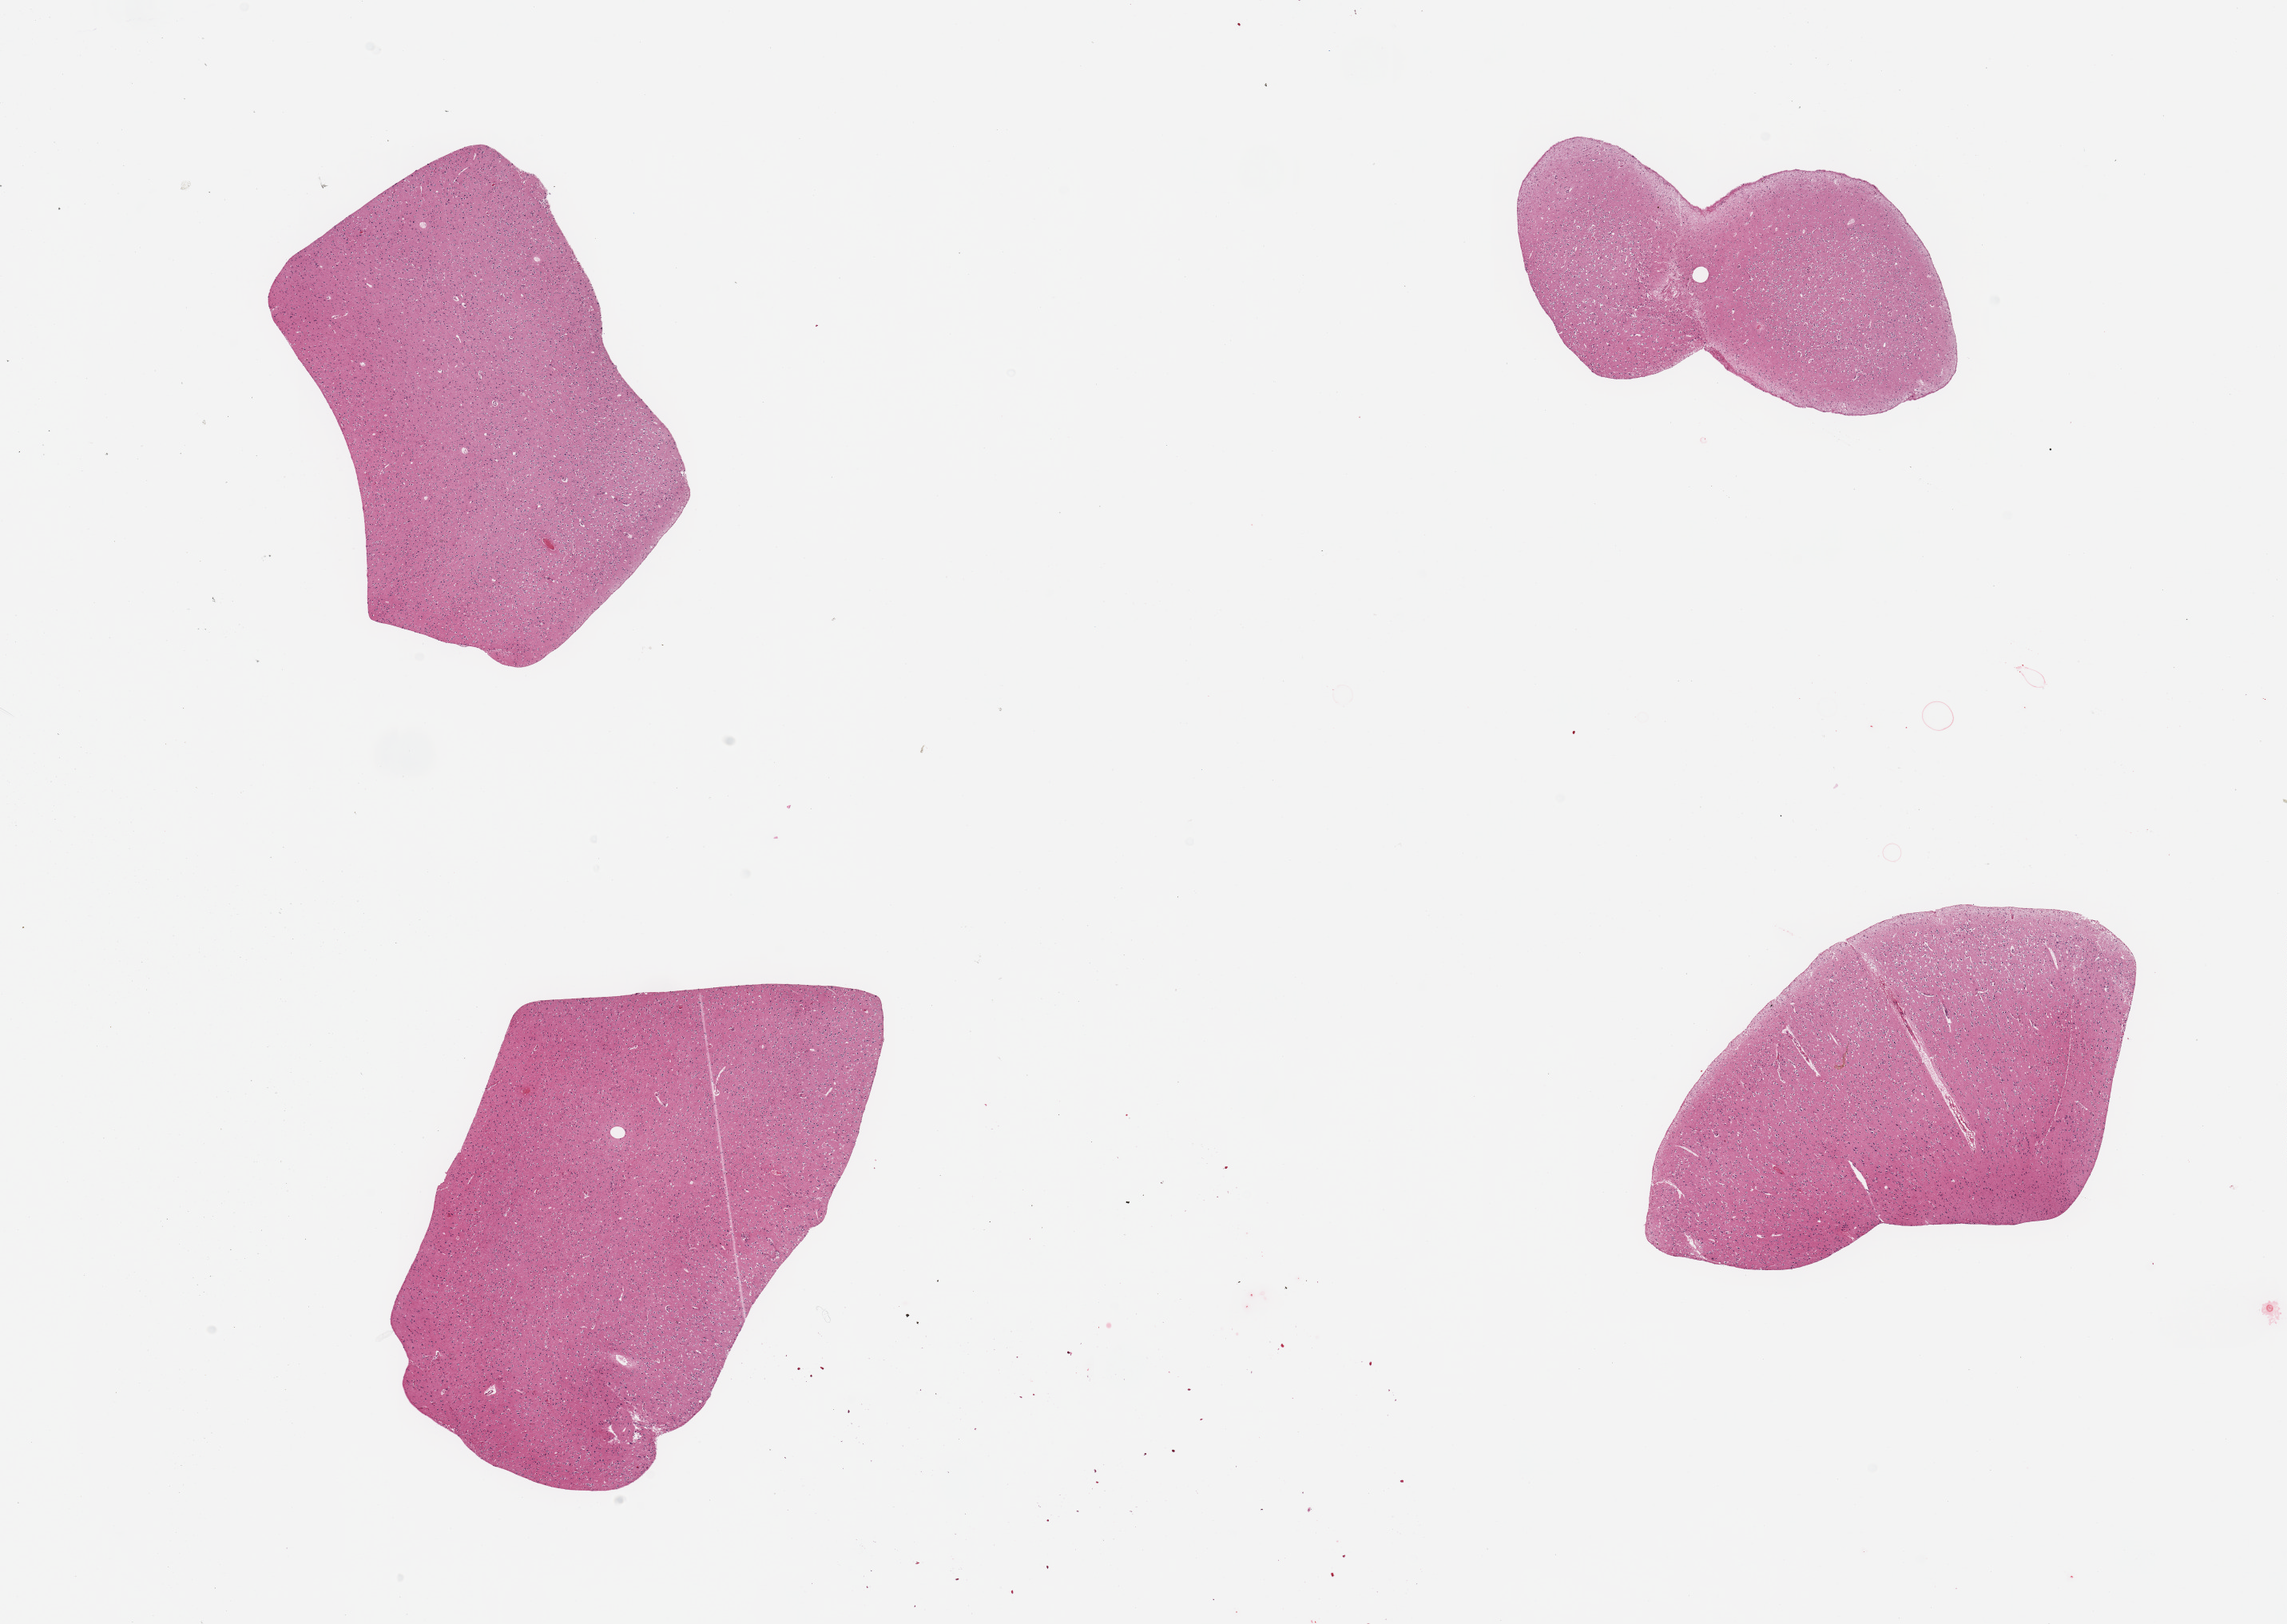
Hematoxylin and eosin (H&E) whole-slide image, brightfield — shown as a low-resolution overview of the whole scanned area (about 22.6 x 16.1 mm). PAXgene-fixed paraffin-embedded (PFPE) section. Target tissue: cerebral cortex. Donor tissue sample. Donor: female.
• reviewer comment on this tissue sample: 4 pieces